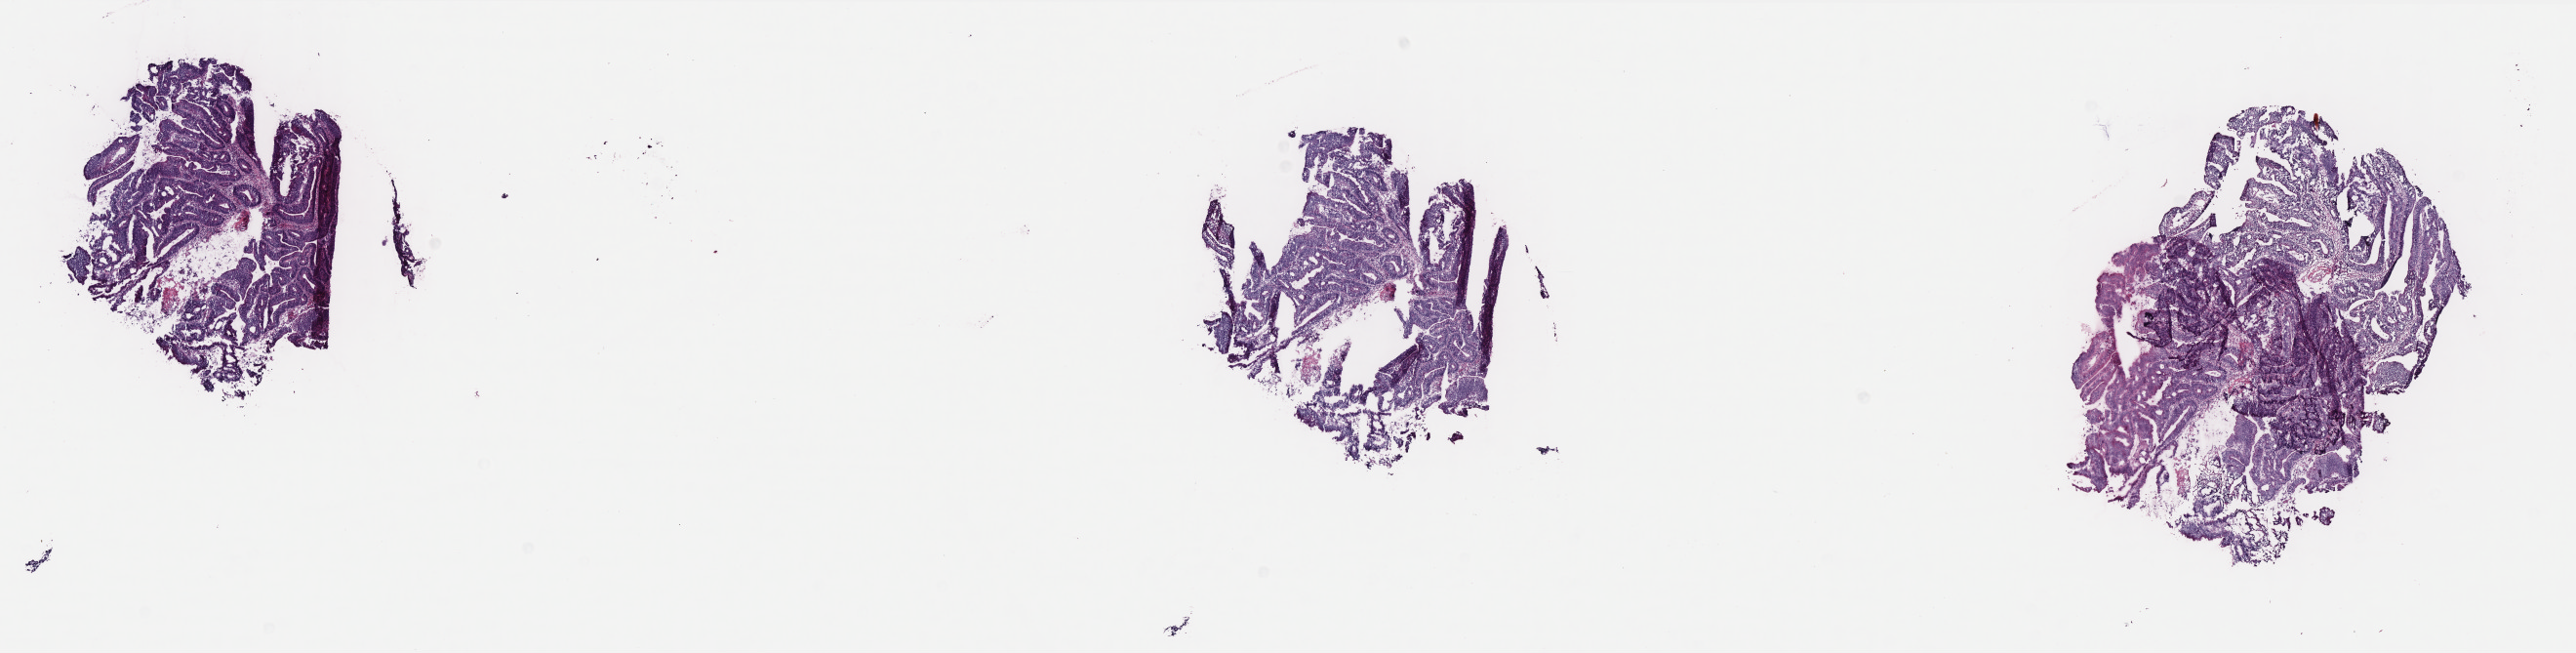
Hematoxylin and eosin (H&E) stained whole-slide image, shown as a low-resolution overview of the whole scanned area (about 21.2 x 5.4 mm), frozen section from the bottom of the tissue portion, colon, primary tumour sample. Patient: female, age at initial diagnosis 66 years. Composition of this section per pathologist review: tumour cells 99%, tumour nuclei 85%, normal cells 0%, stromal cells 0%, necrosis 1%. Infiltration values recorded for this section: lymphocyte infiltration 4%, monocyte infiltration 1%, neutrophil infiltration 2%.
- AJCC pathologic stage: IIIB (6th edition)
- diagnosis: Adenocarcinoma, NOS (sigmoid colon)